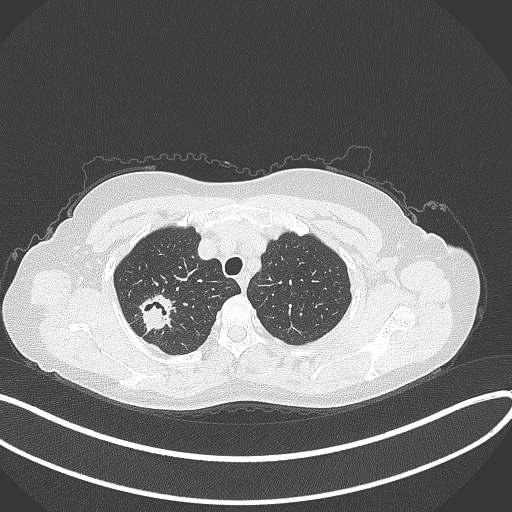
Chest CT, one axial slice. Slice 302 of 337 in the series (ordered by position). Reconstruction kernel B70f. Lung window (W 1500 / L -600 HU). 1 mm slice thickness. 512 × 512 image matrix, field of view 400 × 400 mm. Female patient, age 50 years. From the clinical record (not read from this slice): clinical TNM (as recorded): T1c N0 M0; histopathological grade: G2-3.
Structures marked on this image (bounding box drawn by a radiologist):
- lung tumour (recorded histology: adenocarcinoma): bounding box (x1, y1, x2, y2) in pixels: (133, 289, 183, 335)